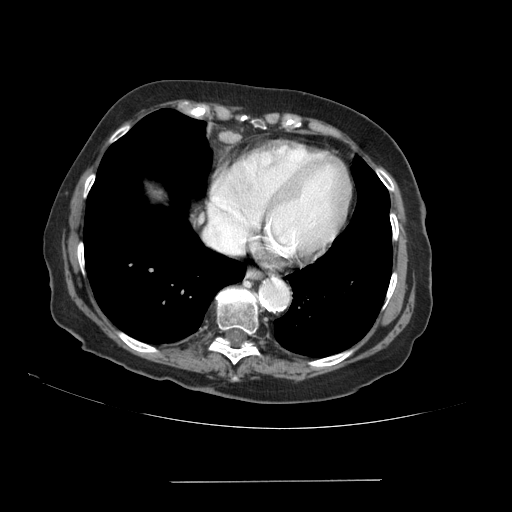
Contrast-enhanced abdominal CT (liver protocol), one axial slice; position 85 of 89 along the scan axis; 140 kVp; soft-tissue window (W 400 / L 40 HU); 2.5 mm slice thickness; 512 × 512 image matrix. Case-level facts recorded for this patient, not image findings: diagnosis: hepatocellular carcinoma (patient treated with transarterial chemoembolisation; whether this scan precedes or follows treatment is not stated here); TNM stage (as recorded): Stage-IVA.
Annotated regions visible in this slice (semi-automatic segmentation, software-assisted and operator-edited):
- liver parenchyma outside the tumour (the mass and vessels are separate outlines, so this box may not span the whole liver): box from (x=148, y=184) to (x=165, y=200) px